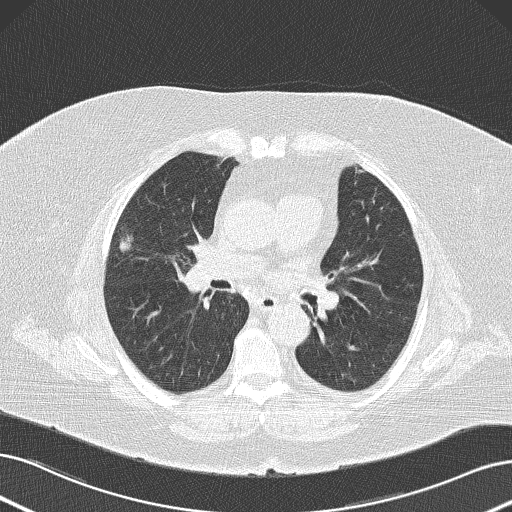
Low-dose screening chest CT, axial slice; baseline annual screen; lung window (W 1500 / L -600 HU); slice 70 of 145 in the series; 512 × 512 image matrix. Female, age 73 years at enrolment.
Expert reader's lesion annotation, bounding box [x1, y1, x2, y2] px = [99, 218, 145, 262]. The exam's reader record, not a measurement of the box and not confirmed to be the same lesion: non-calcified nodule or mass ≥4 mm, right upper lobe, 15 × 11 mm, poorly defined margins, soft tissue attenuation.